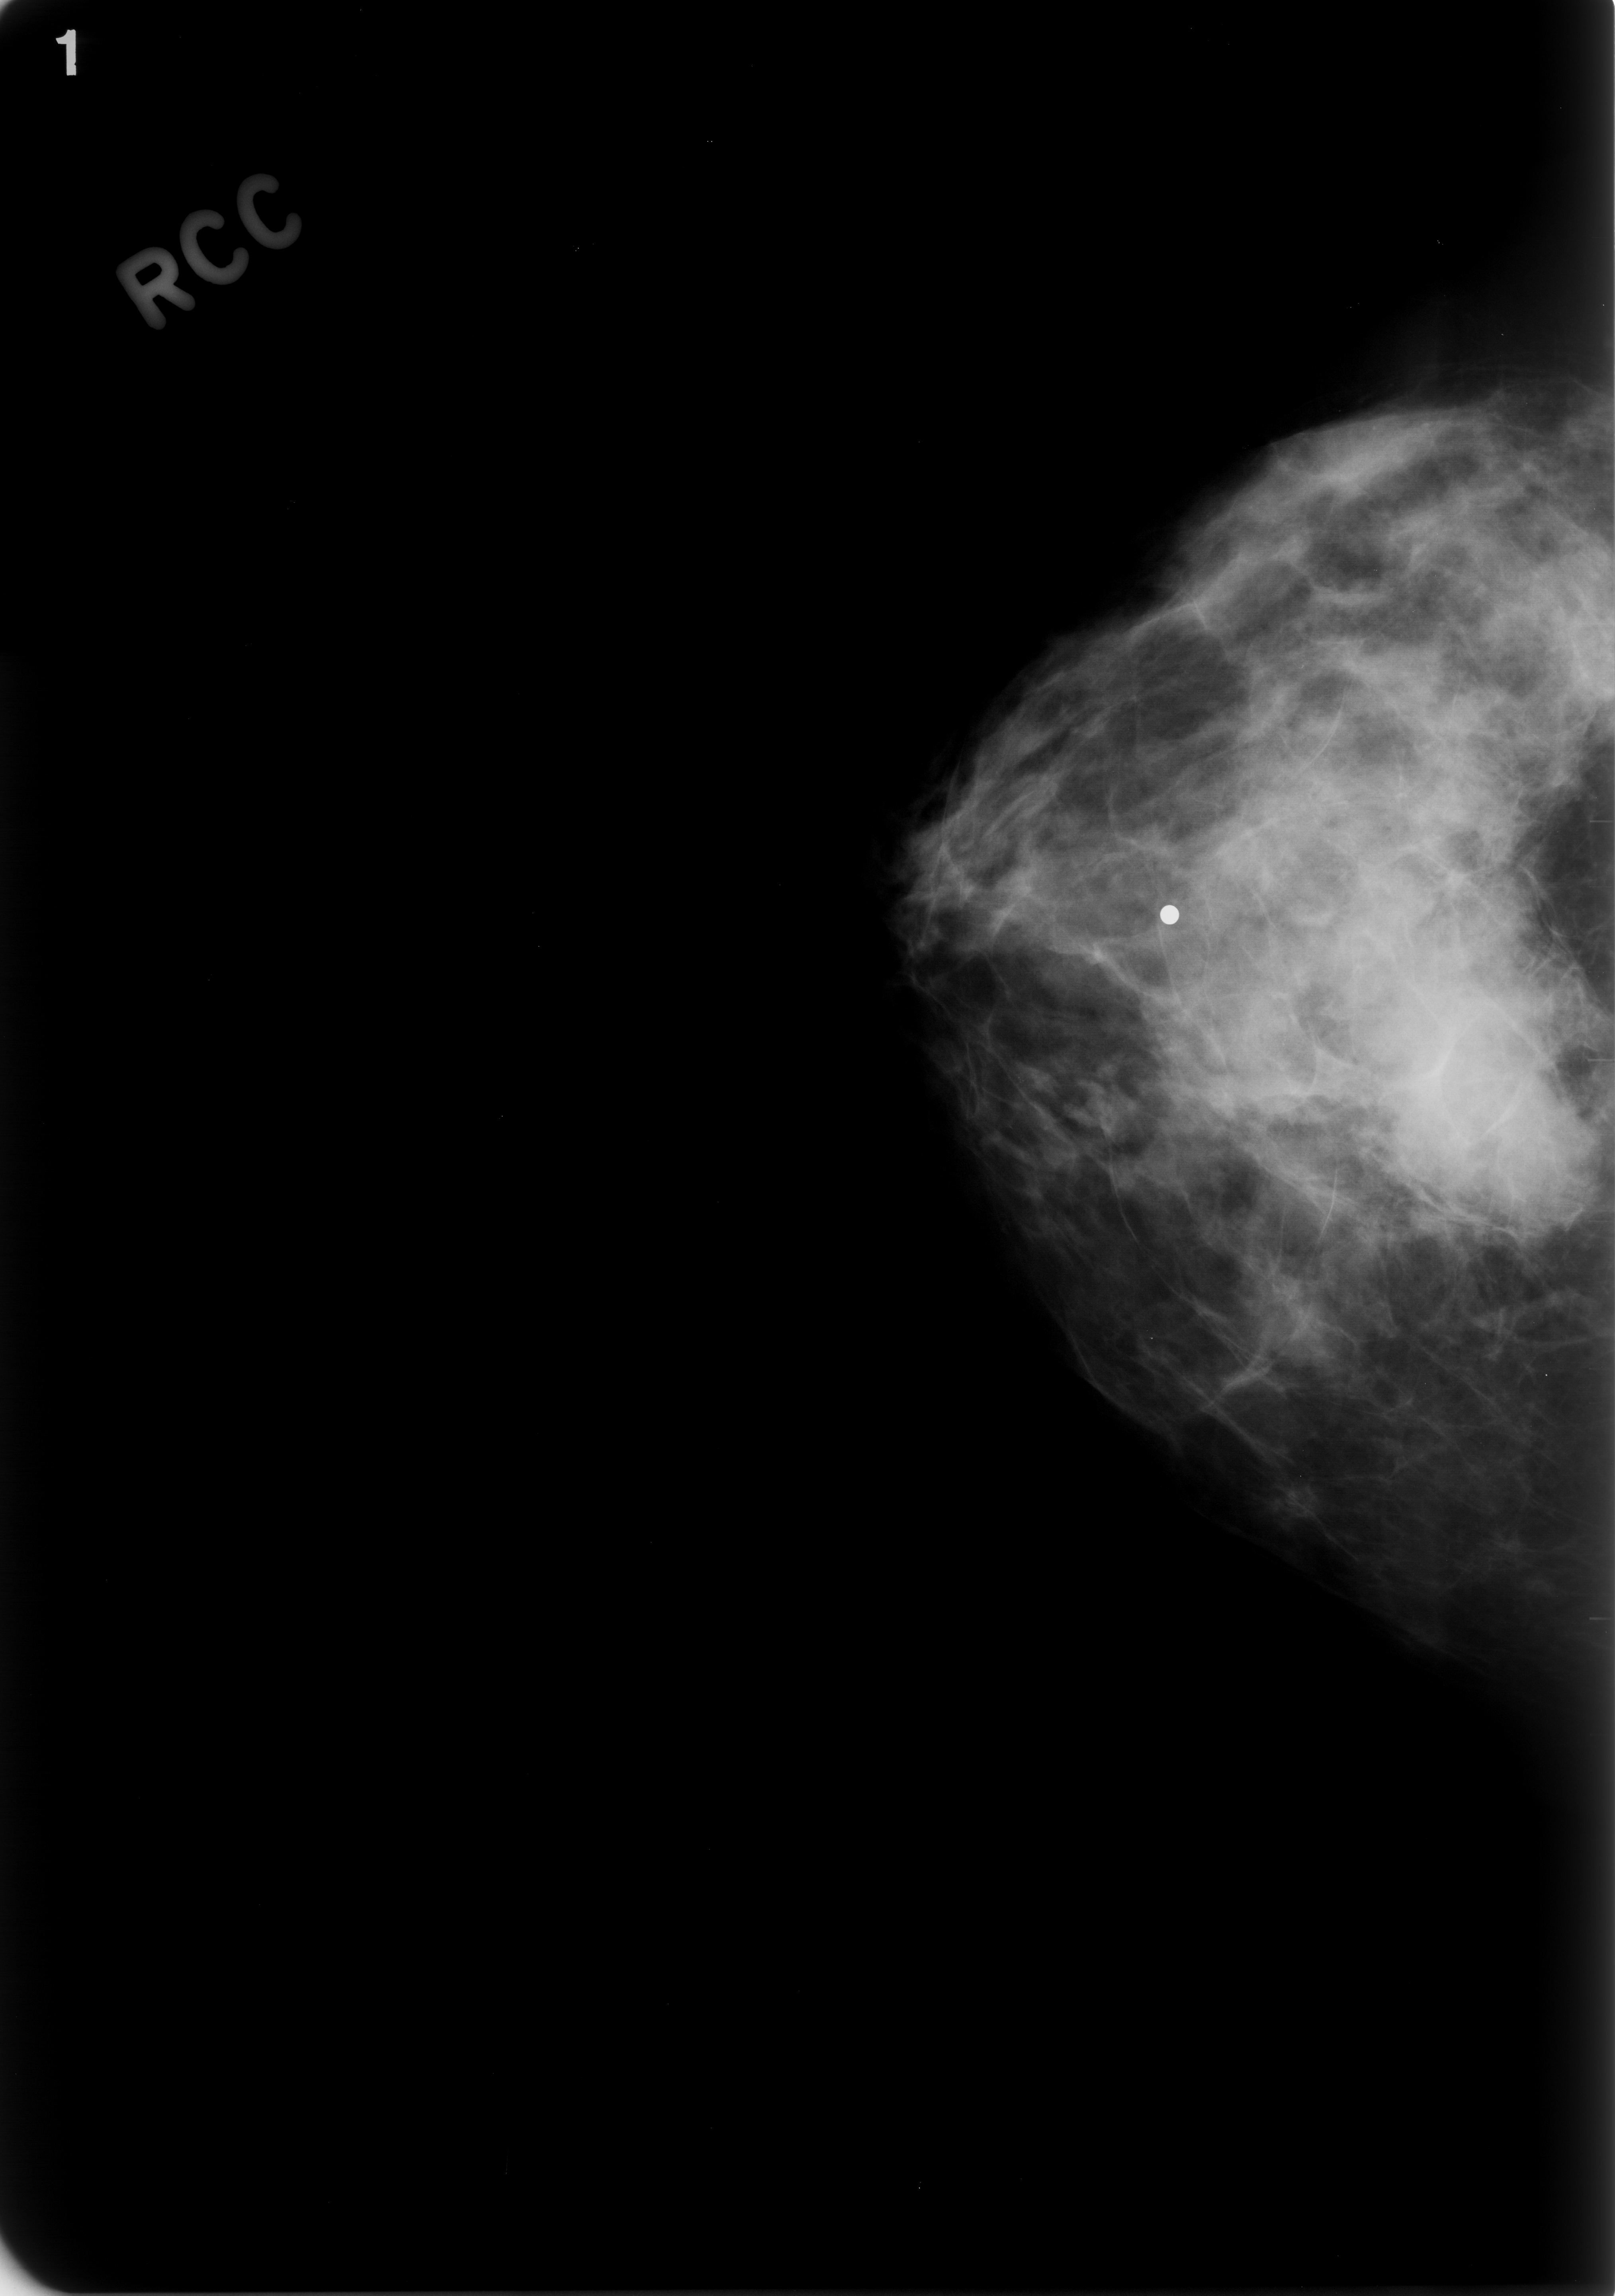
Mammogram (digitized film), right breast, CC view, BI-RADS breast density category 2 (scale 1–4).
Mass, shape asymmetric breast tissue, margins ill defined; BI-RADS assessment category 5; pathology result (as recorded, not read from the image): malignant.